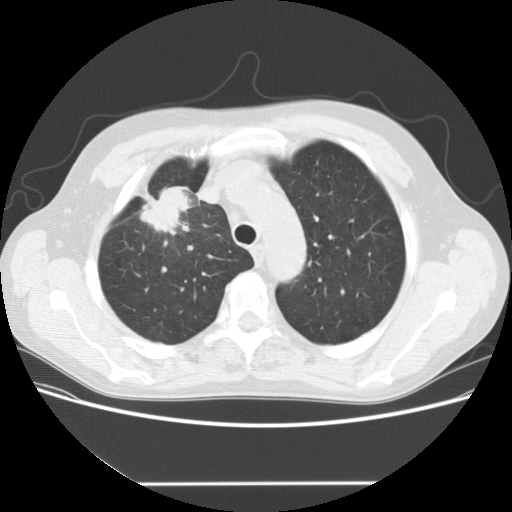
Low-dose screening chest CT, one axial slice. Position 121 of 153 along the scan axis. Lung window (W 1500 / L -600 HU). 2.5 mm slice thickness. 512 × 512 image matrix.
Annotated regions visible in this slice (manually delineated by an expert):
- lesion 1 (tumor, upper lobe of right lung): box from (x=140, y=186) to (x=193, y=235) px